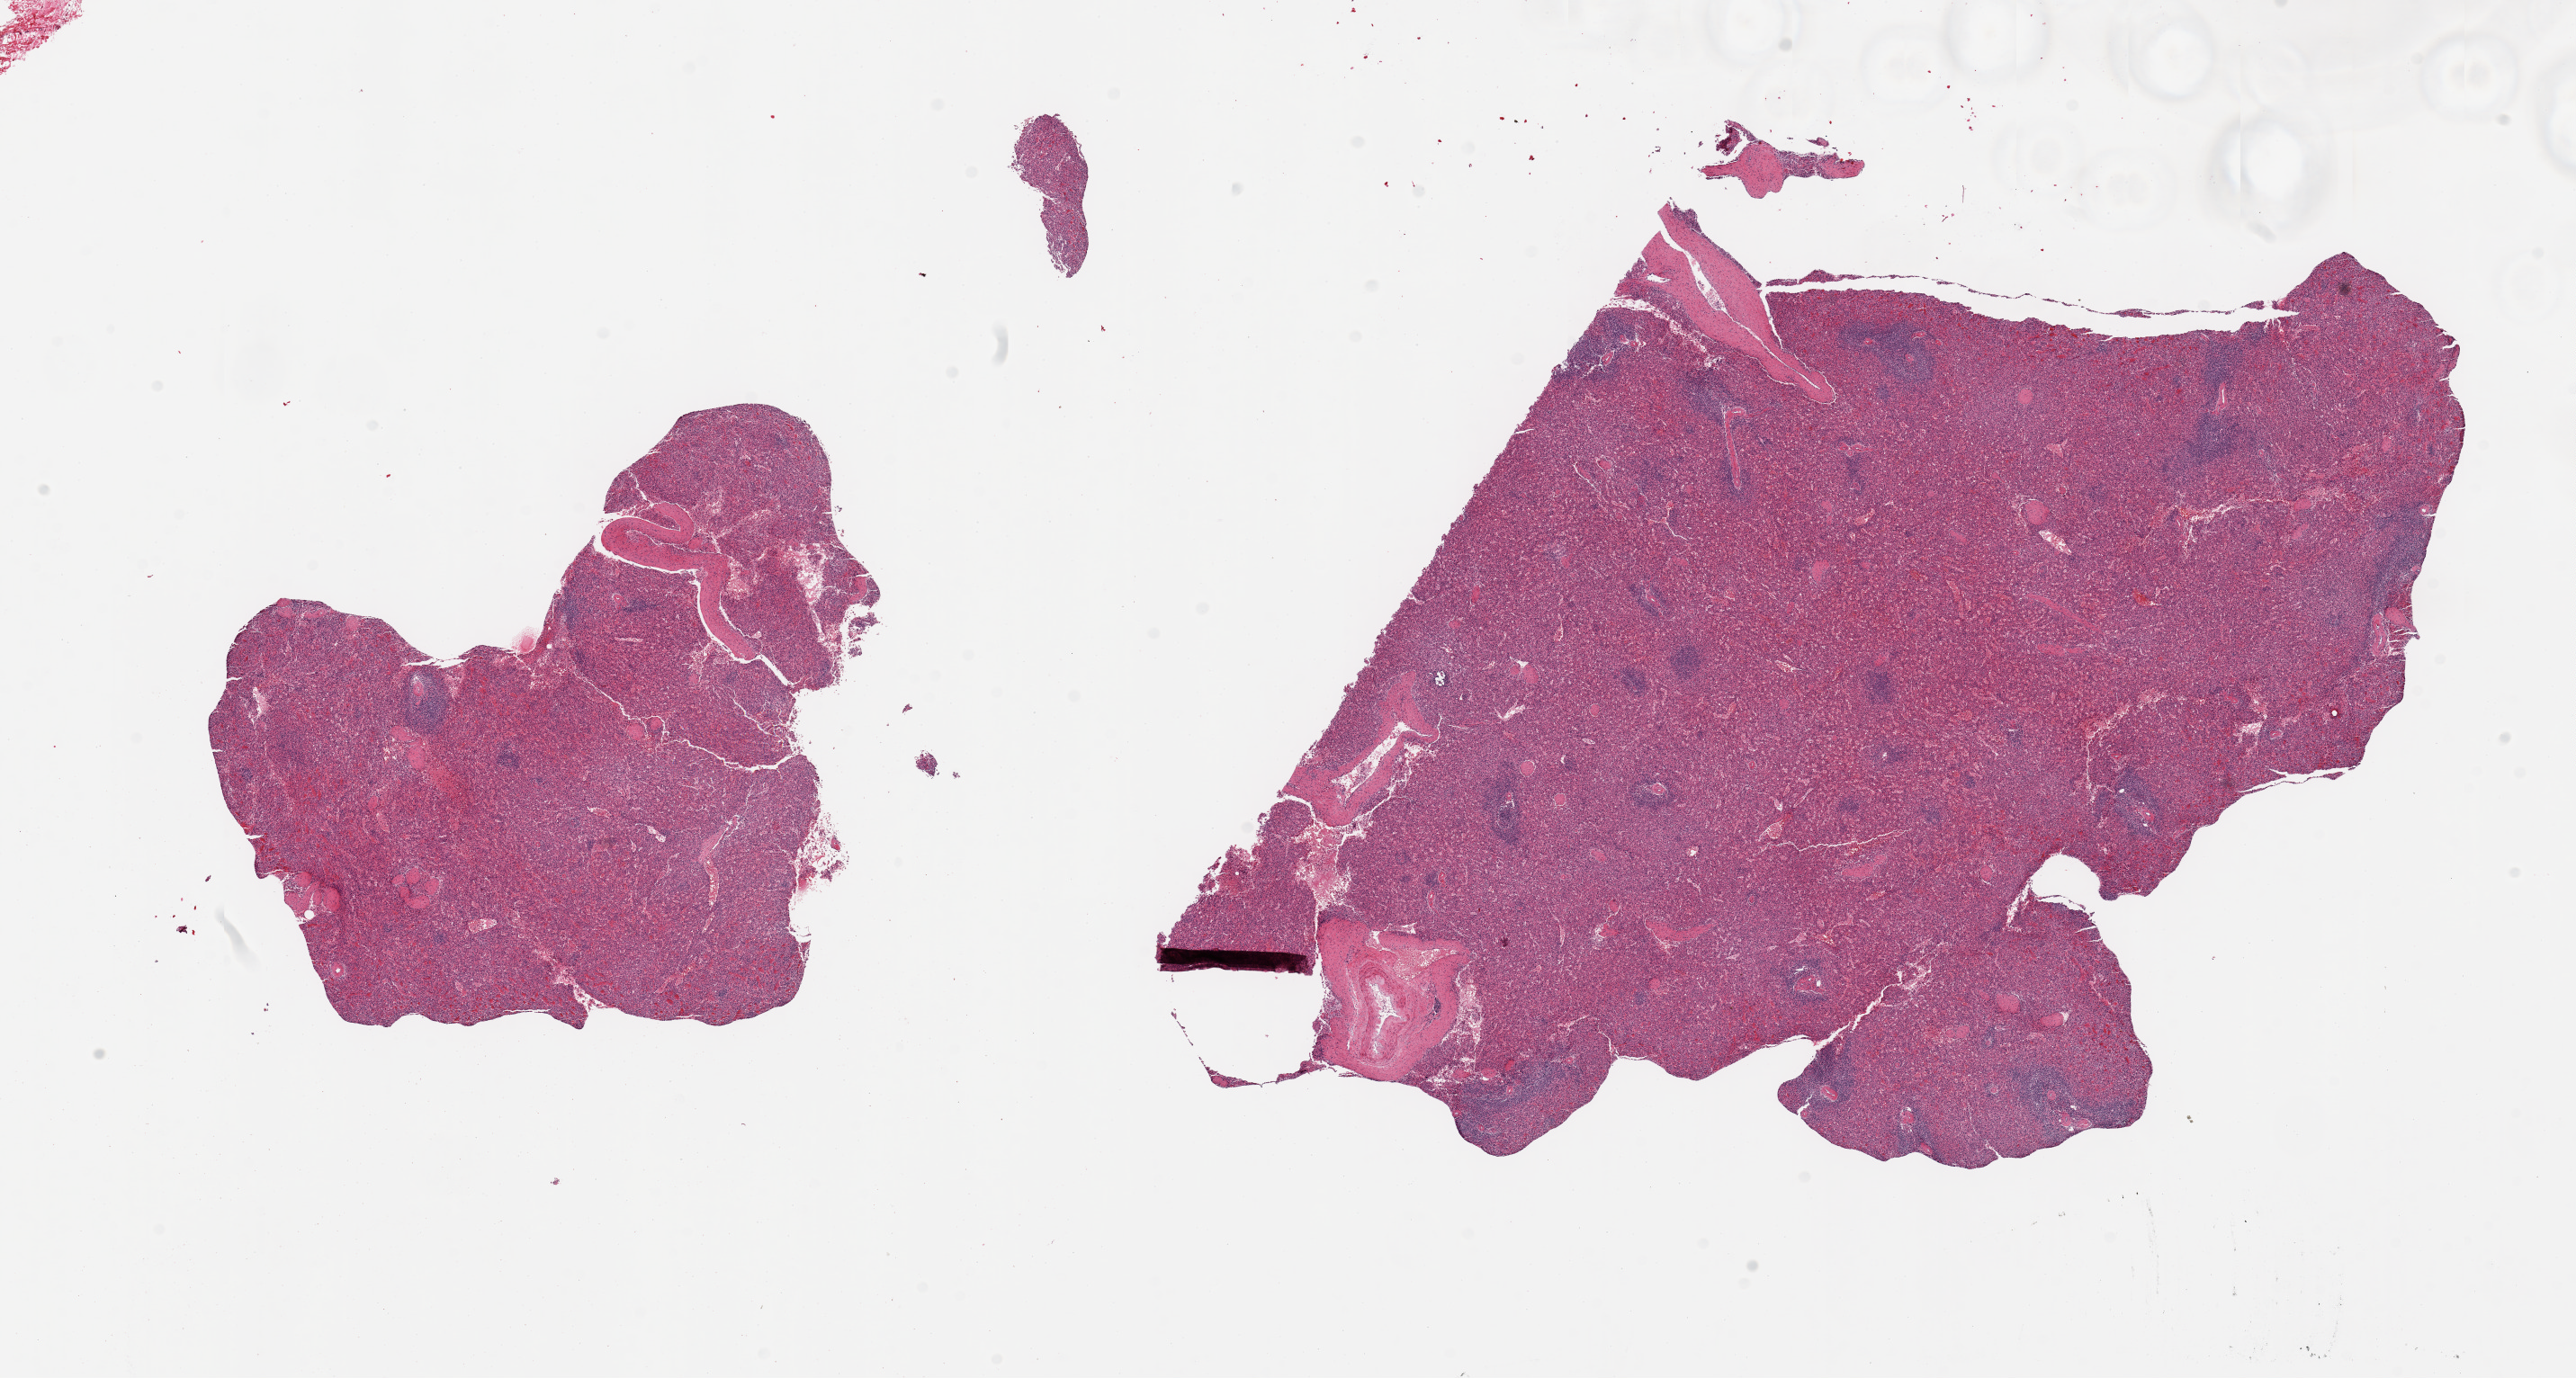
H&E whole-slide image — a low-resolution overview of the entire scanned area, about 22.6 x 12.1 mm, PAXgene-fixed, paraffin-embedded tissue, target tissue: spleen, tissue donor sample. Donor: male.
Review note (as recorded): 2 pieces.